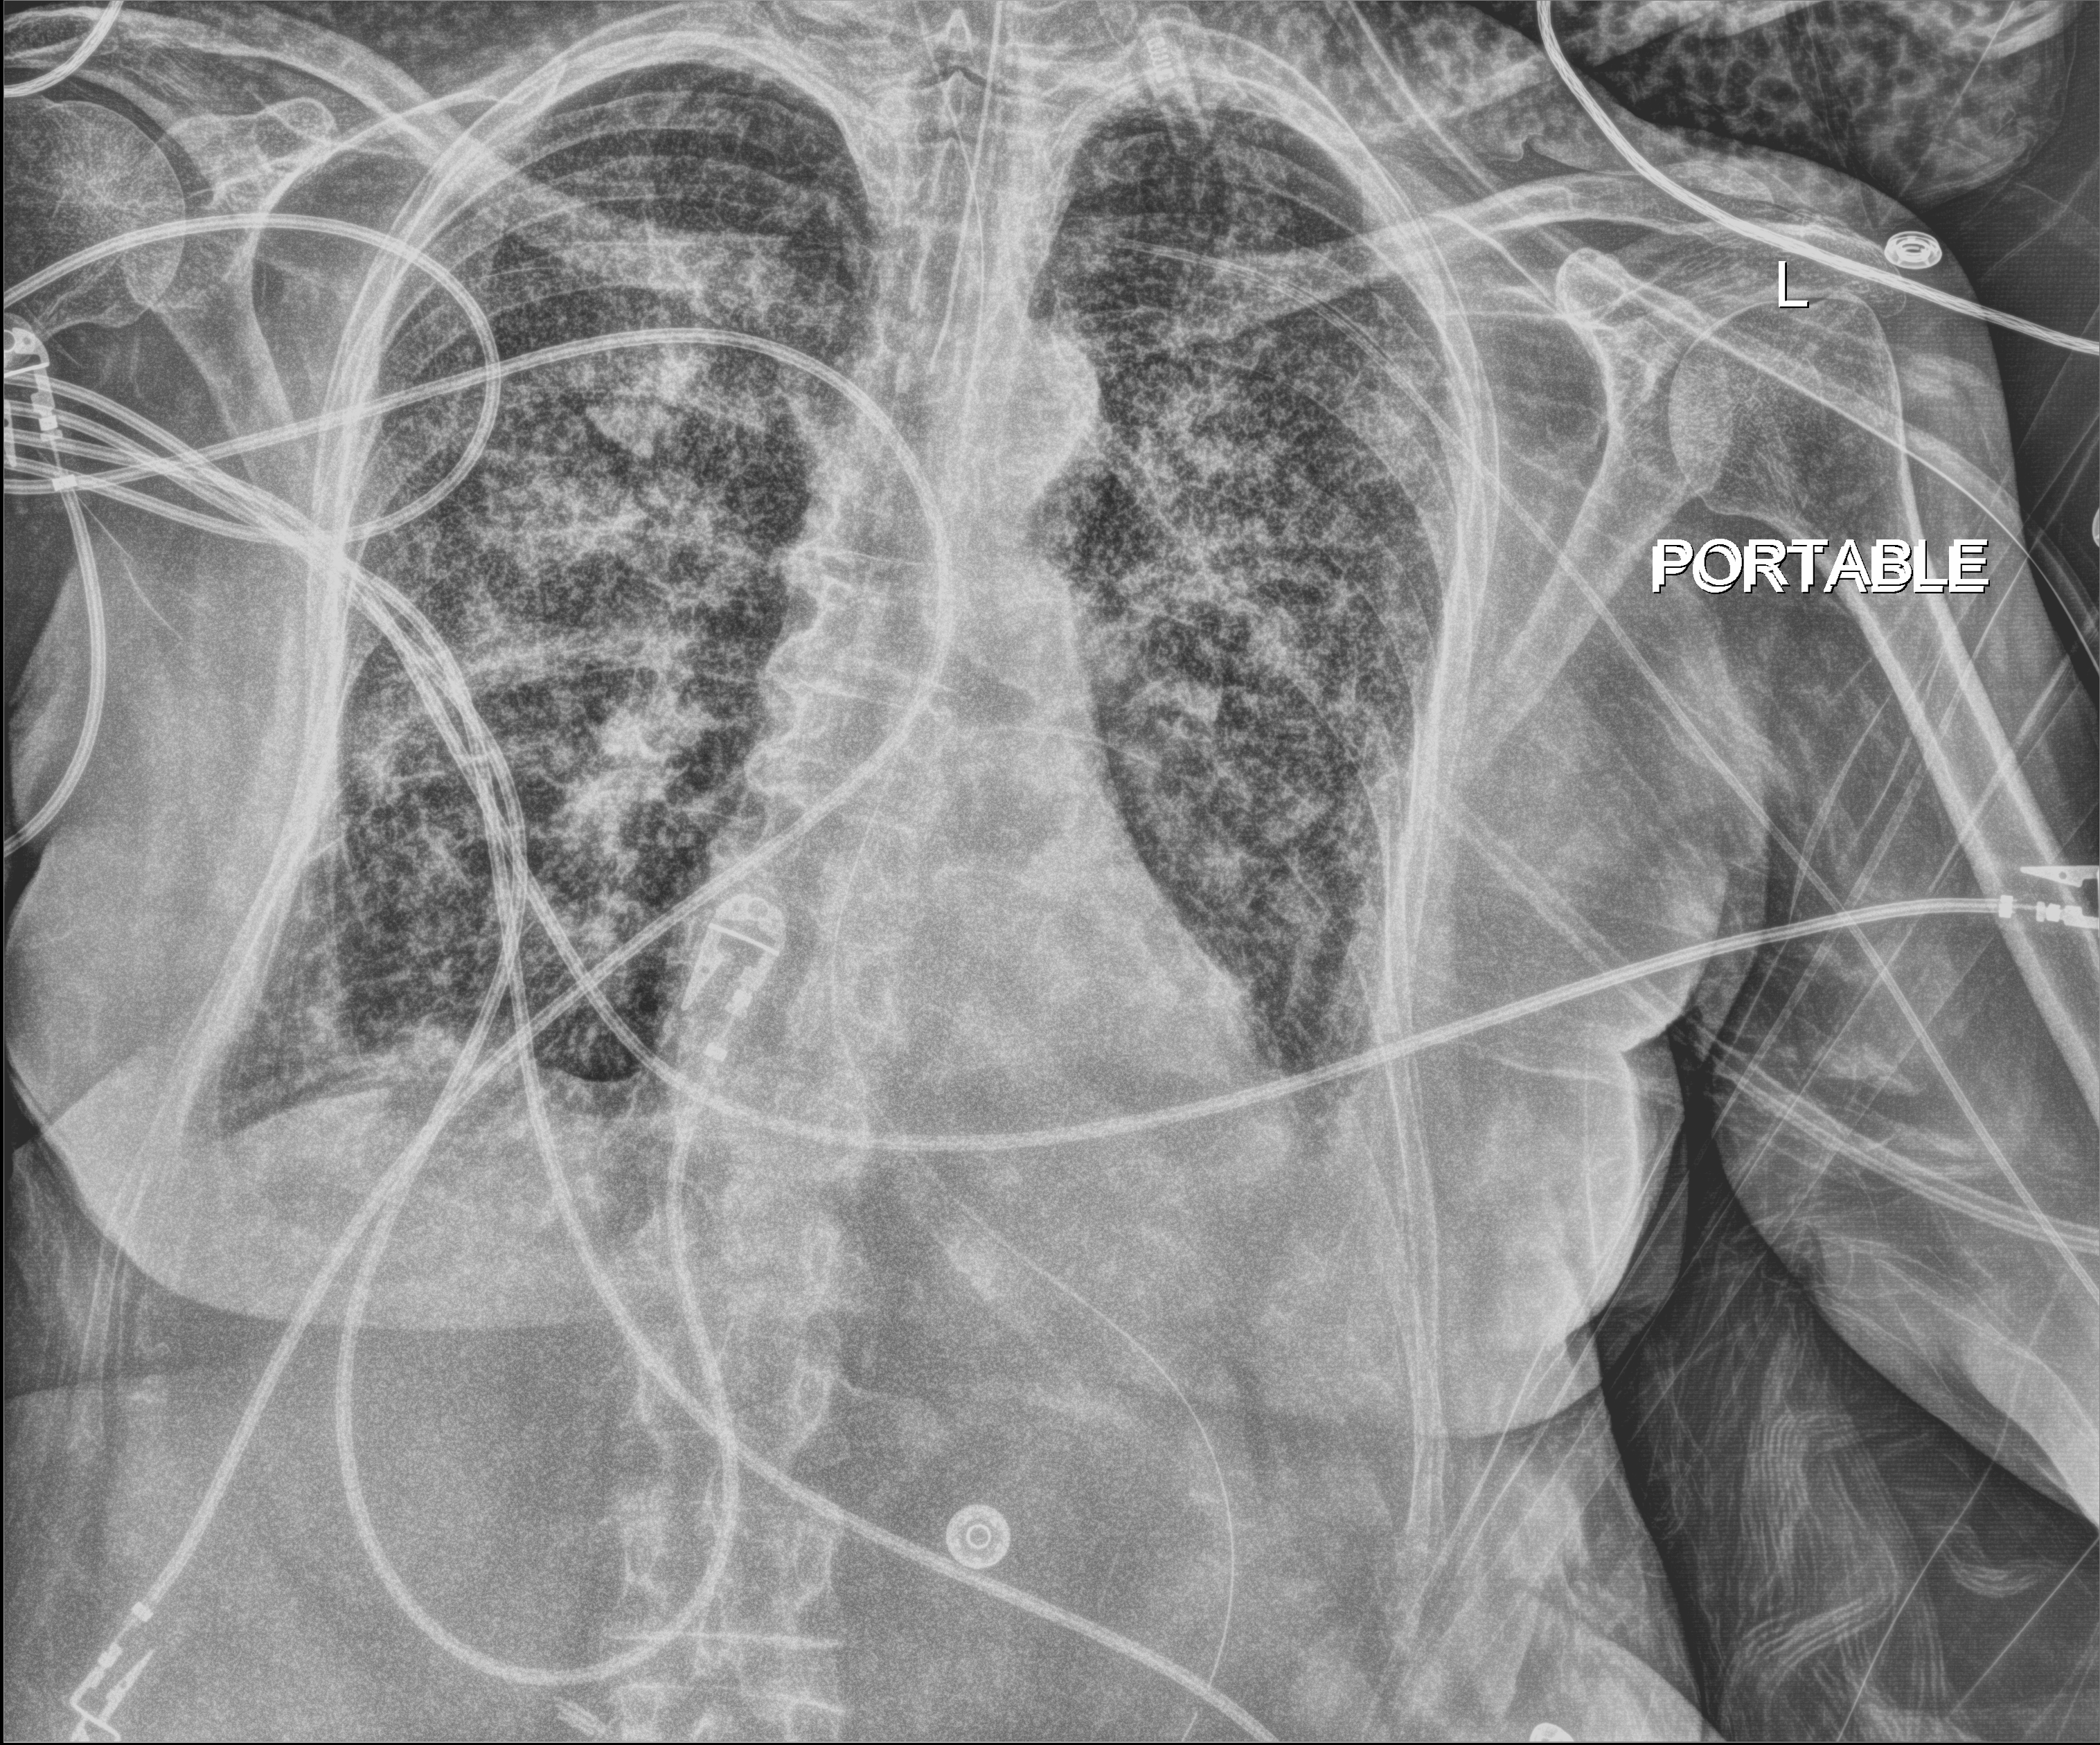
Bedside chest radiograph (digital radiography), anteroposterior (AP) projection. Female patient hospitalised with COVID-19, age 75–90 years.
Admission-level facts for this patient (not findings on this image; timing relative to this image not recorded): mechanically ventilated during this hospital stay: yes.